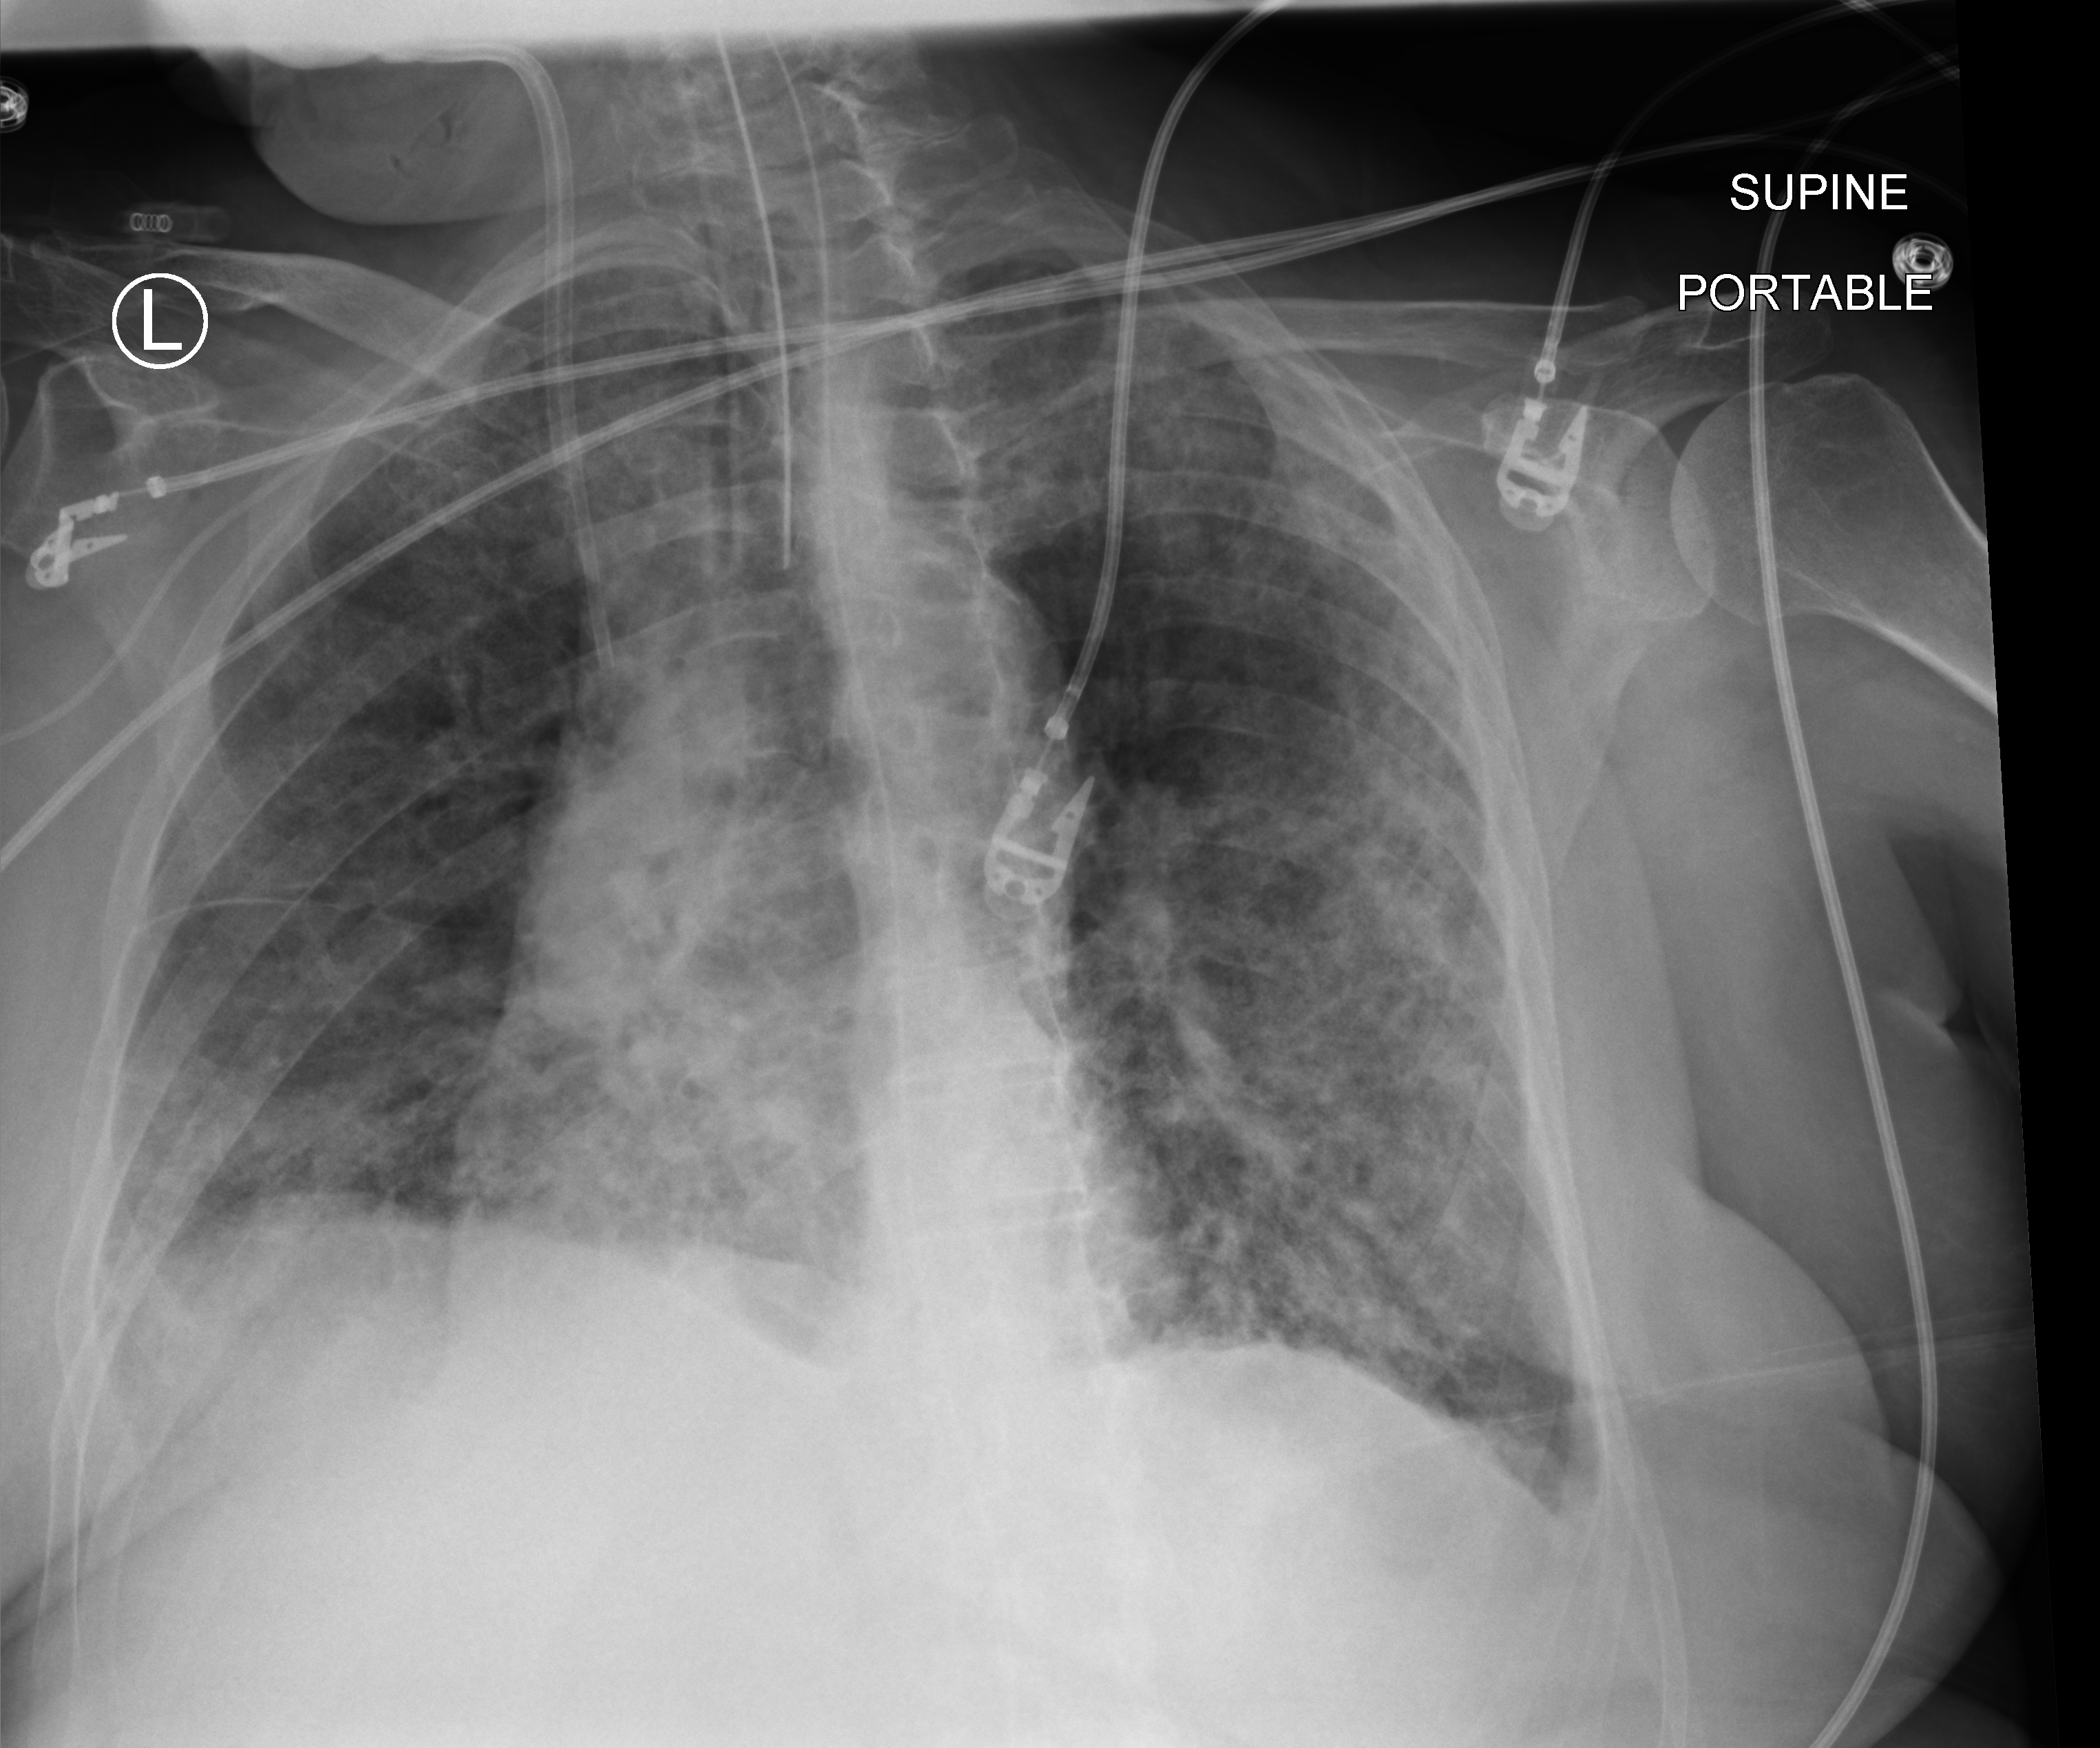
Portable chest radiograph. Patient hospitalised with COVID-19; female, aged 75–90 years.
Hospital-stay facts (about this admission, not read from this image; timing relative to this image not recorded):
- length of hospital stay: 28 days
- admitted to intensive care during this hospital stay: yes